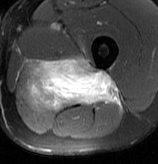
MRI of an extremity soft-tissue mass, one axial slice. Position 46 of 70 along the scan axis. T2-weighted fat-saturated. MR volume resampled by the dataset authors to the PET/CT grid (not the native acquisition matrix). 3.27 mm slice thickness. 158 × 164 image matrix. Male patient. Case-level facts recorded for this patient, not image findings: histological type: extraskeletal osteosarcoma; grade: high; site of the primary tumour: left adductur.
Outlined on this slice (expert contour drawn on MRI and transferred to this co-registered scan by the dataset authors):
- gross tumour volume (mass): bounding box [x1, y1, x2, y2] px = [26, 53, 119, 111]